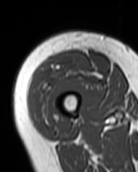
MRI of an extremity soft-tissue mass, one axial slice; MR volume resampled by the dataset authors to the PET/CT grid (not the native acquisition matrix); 138 × 172 image matrix, field of view 135 × 168 mm. Female patient. From the clinical record (not read from this slice): histological type: pleiomorphic undifferentiated sarcoma; grade: high; site of the primary tumour: right quadricep.
Annotated regions visible in this slice (expert contour drawn on MRI and transferred to this co-registered scan by the dataset authors):
- gross tumour volume including surrounding oedema: bounding box [x1, y1, x2, y2] px = [30, 57, 90, 124]